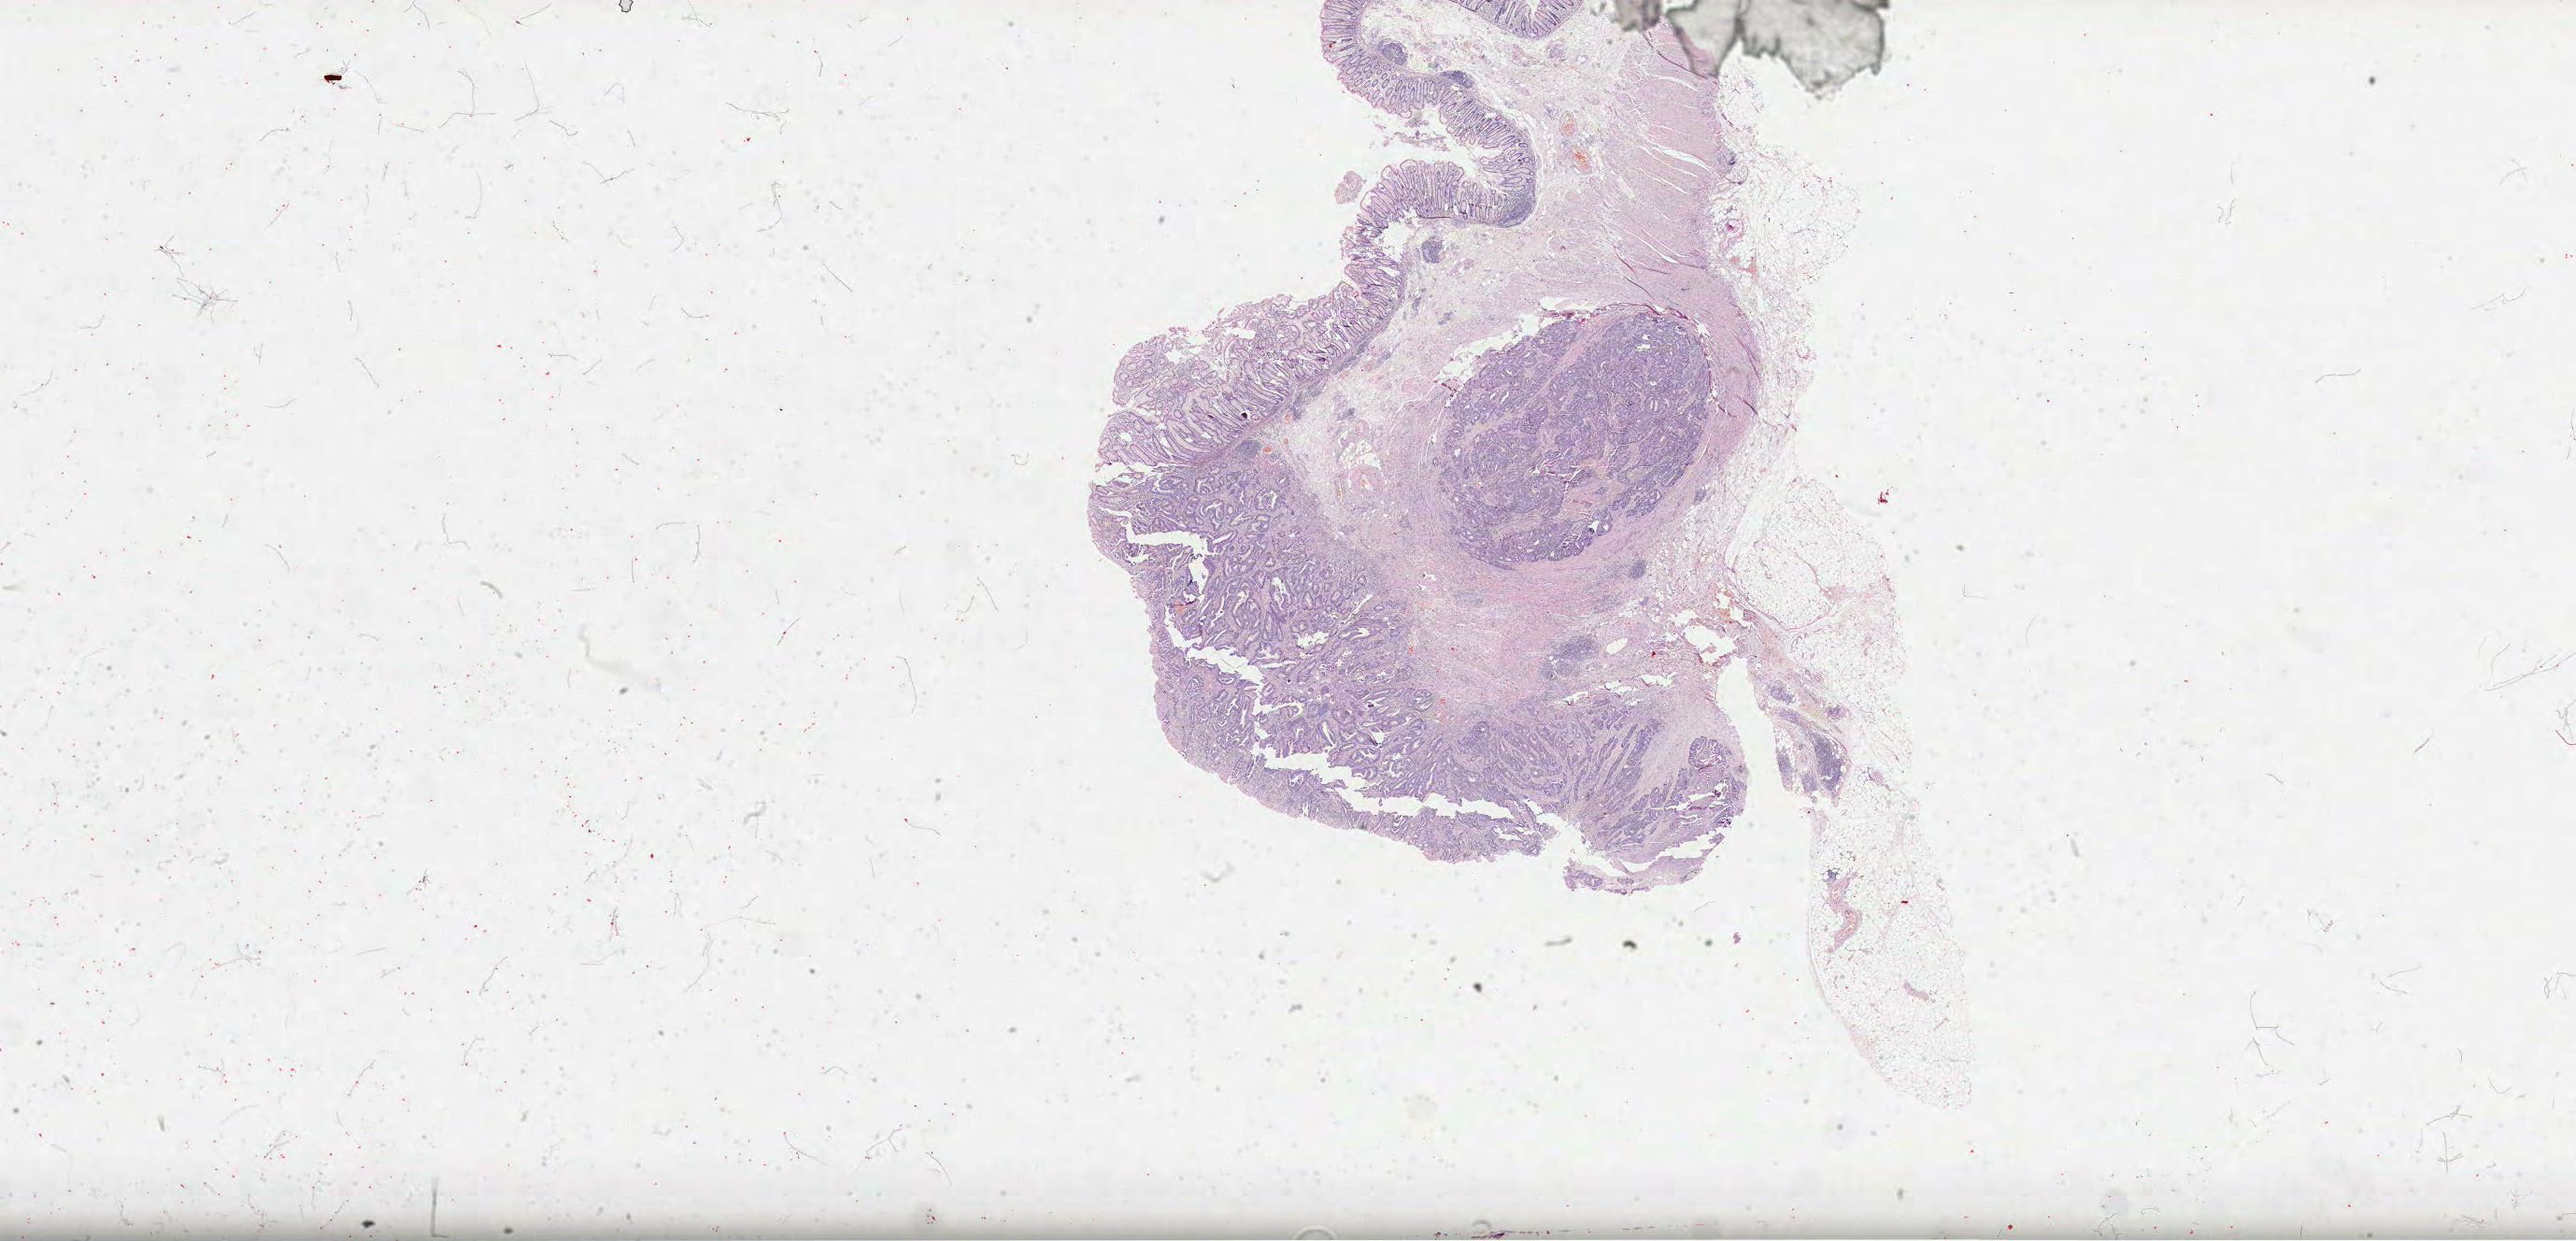
H&E whole-slide image — whole scanned area (about 44.5 x 21.4 mm) shown as a low-resolution overview, FFPE section, colon, primary tumour sample. Male, age 73 years at initial diagnosis.
AJCC pathologic stage: IIA. Histologic diagnosis: Adenocarcinoma, NOS (cecum). TNM: T3 N0 M0.